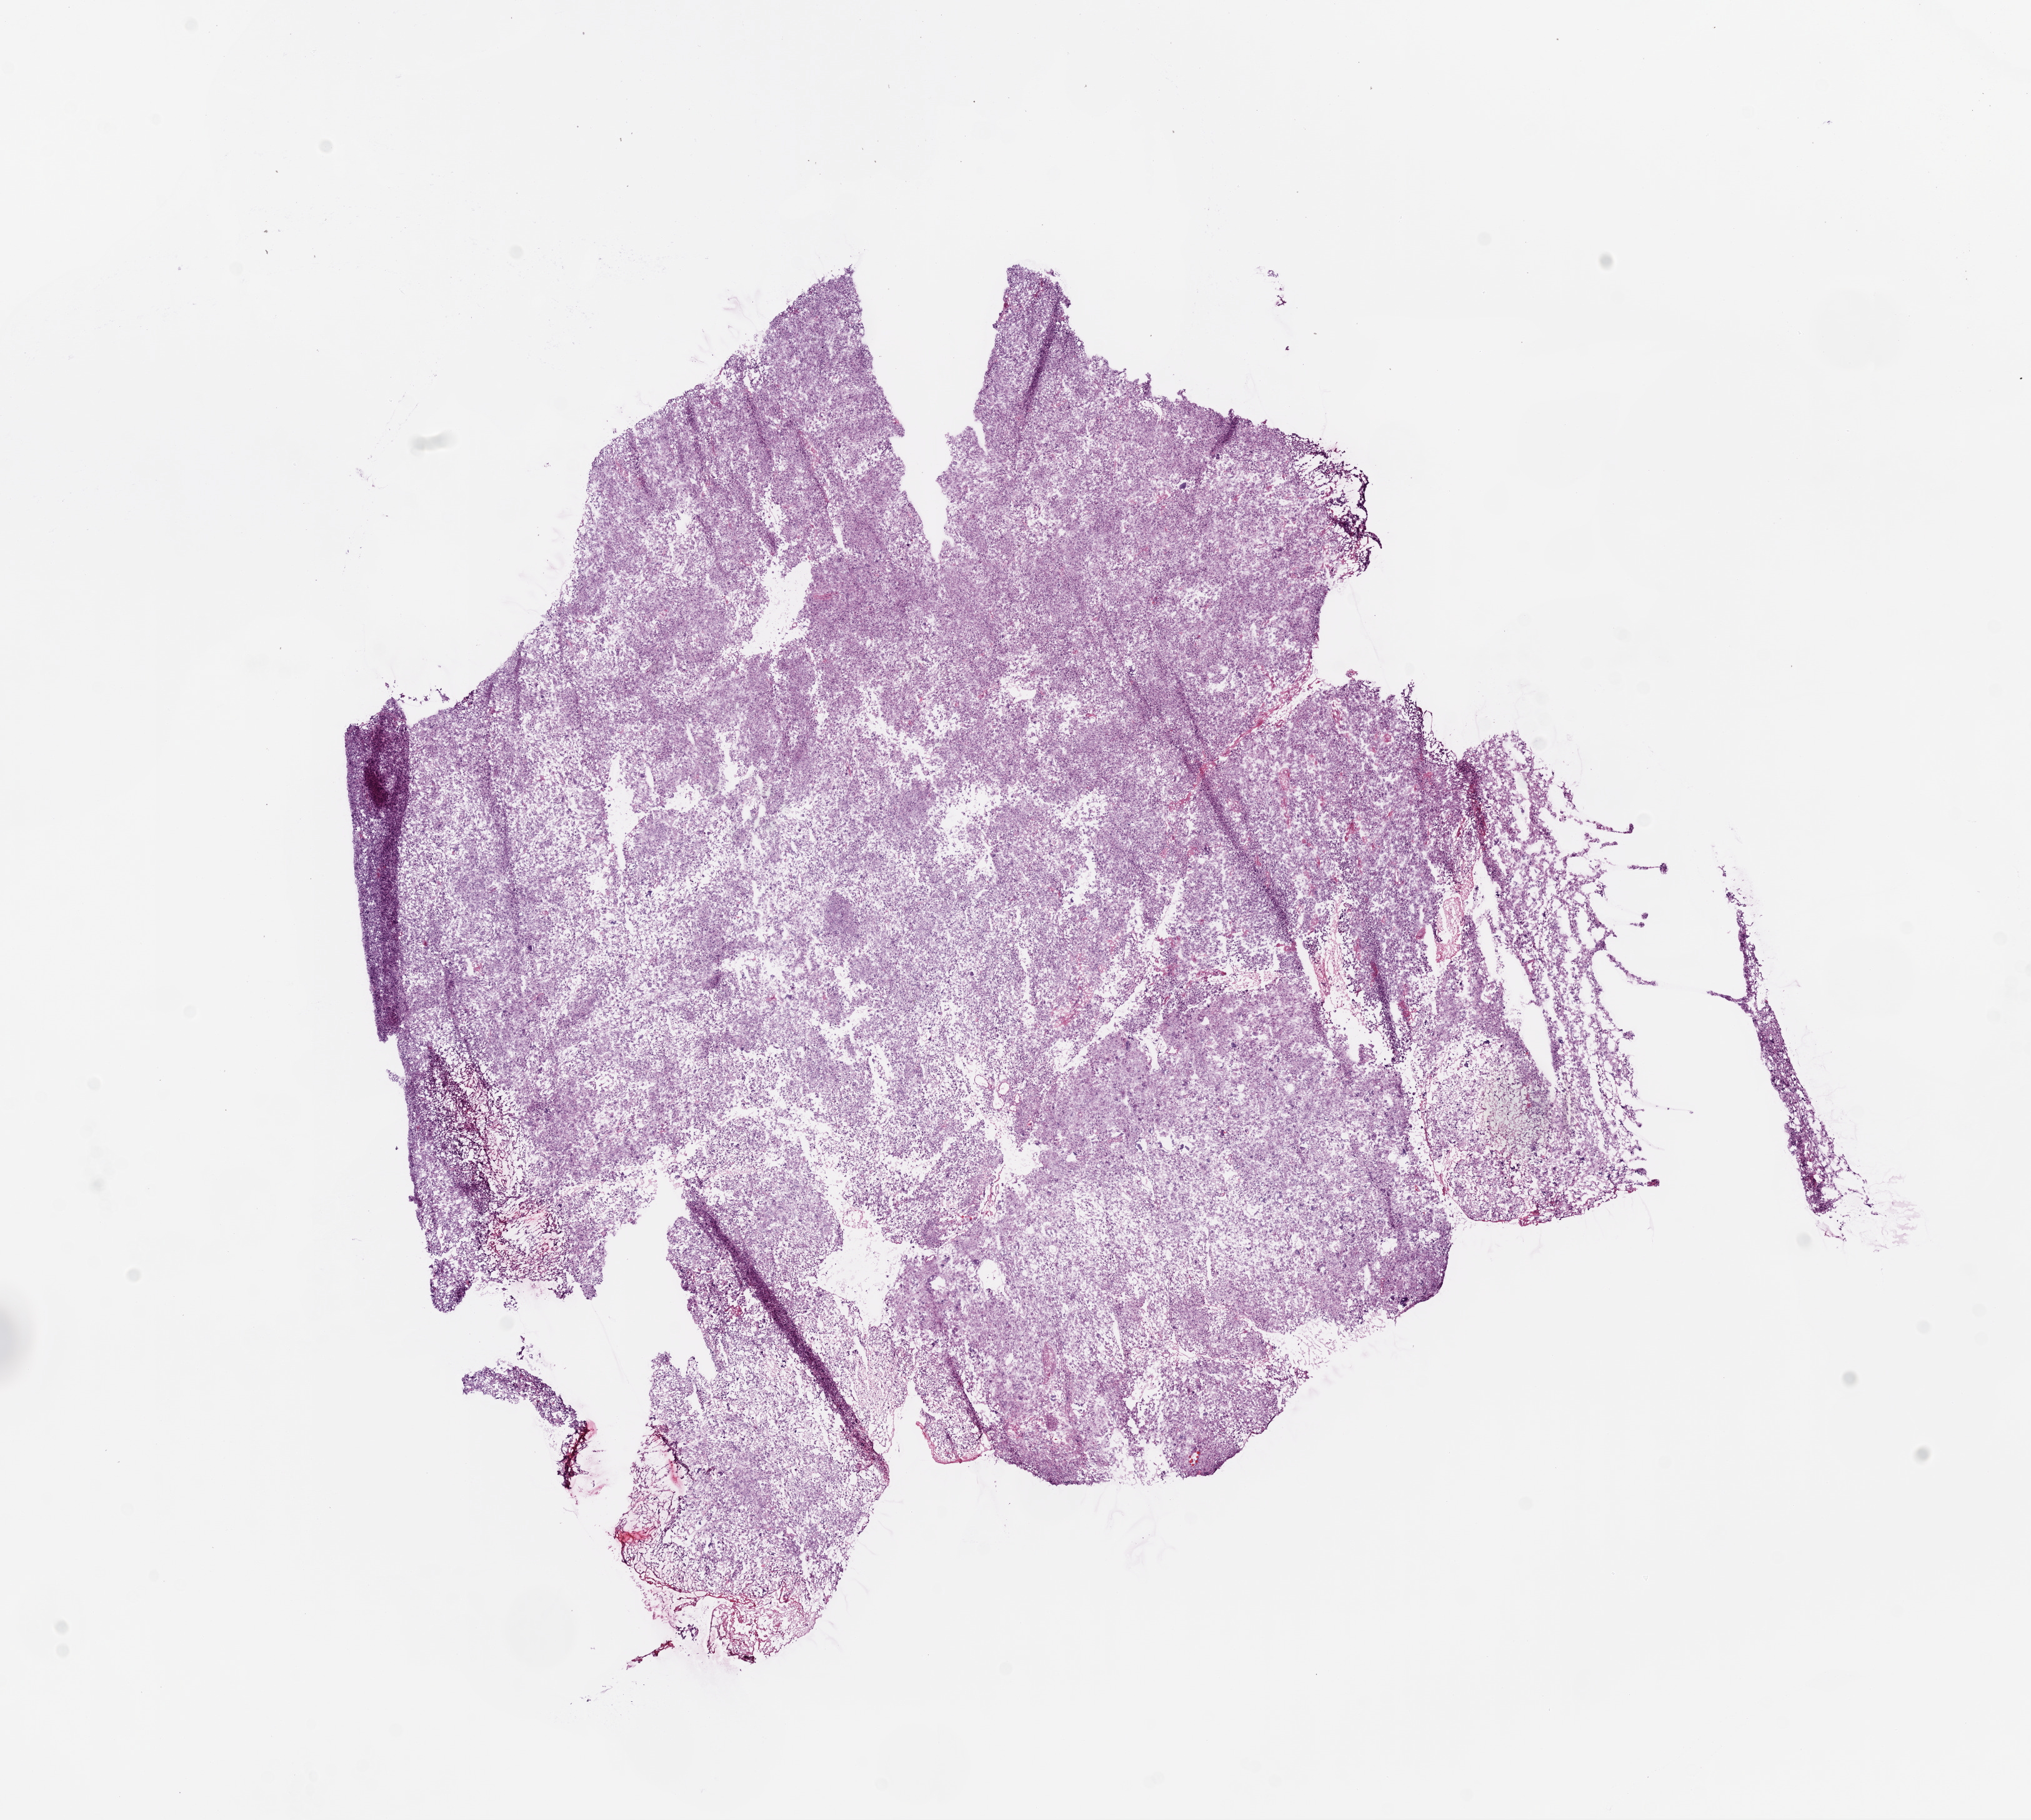
Whole-slide histology image, Hematoxylin and eosin (H&E) stained, low-resolution overview of the scanned area, about 13.0 x 11.7 mm. Frozen section. Primary tumour sample from the brain. Patient: female, age at initial diagnosis 24 years. Slide review estimates, as recorded: tumour cells 100%, tumour nuclei 85%.
Pathologic diagnosis: Glioblastoma.